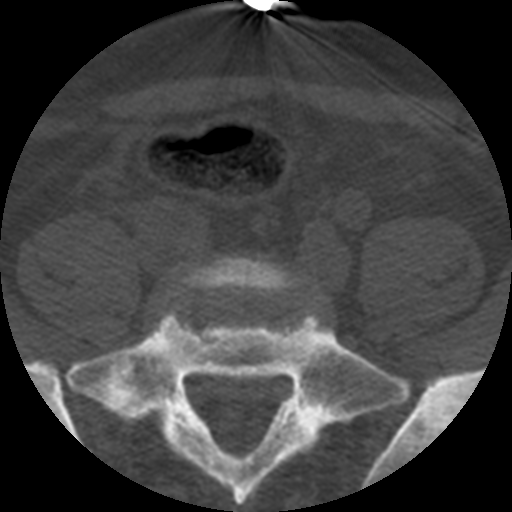
CT including the spine, one axial slice; position 47 of 508 along the scan axis; reconstruction kernel STANDARD; bone window (W 1800 / L 400 HU); 1.25 mm slice thickness; 512 × 512 image matrix. Patient age 57 years. Case-level facts recorded for this patient, not image findings: primary cancer: prostate.
Annotated regions visible in this slice (semi-automatic segmentation, software-assisted and operator-edited):
- L5 vertebra: bounding box [x1, y1, x2, y2] px = [178, 255, 307, 294]